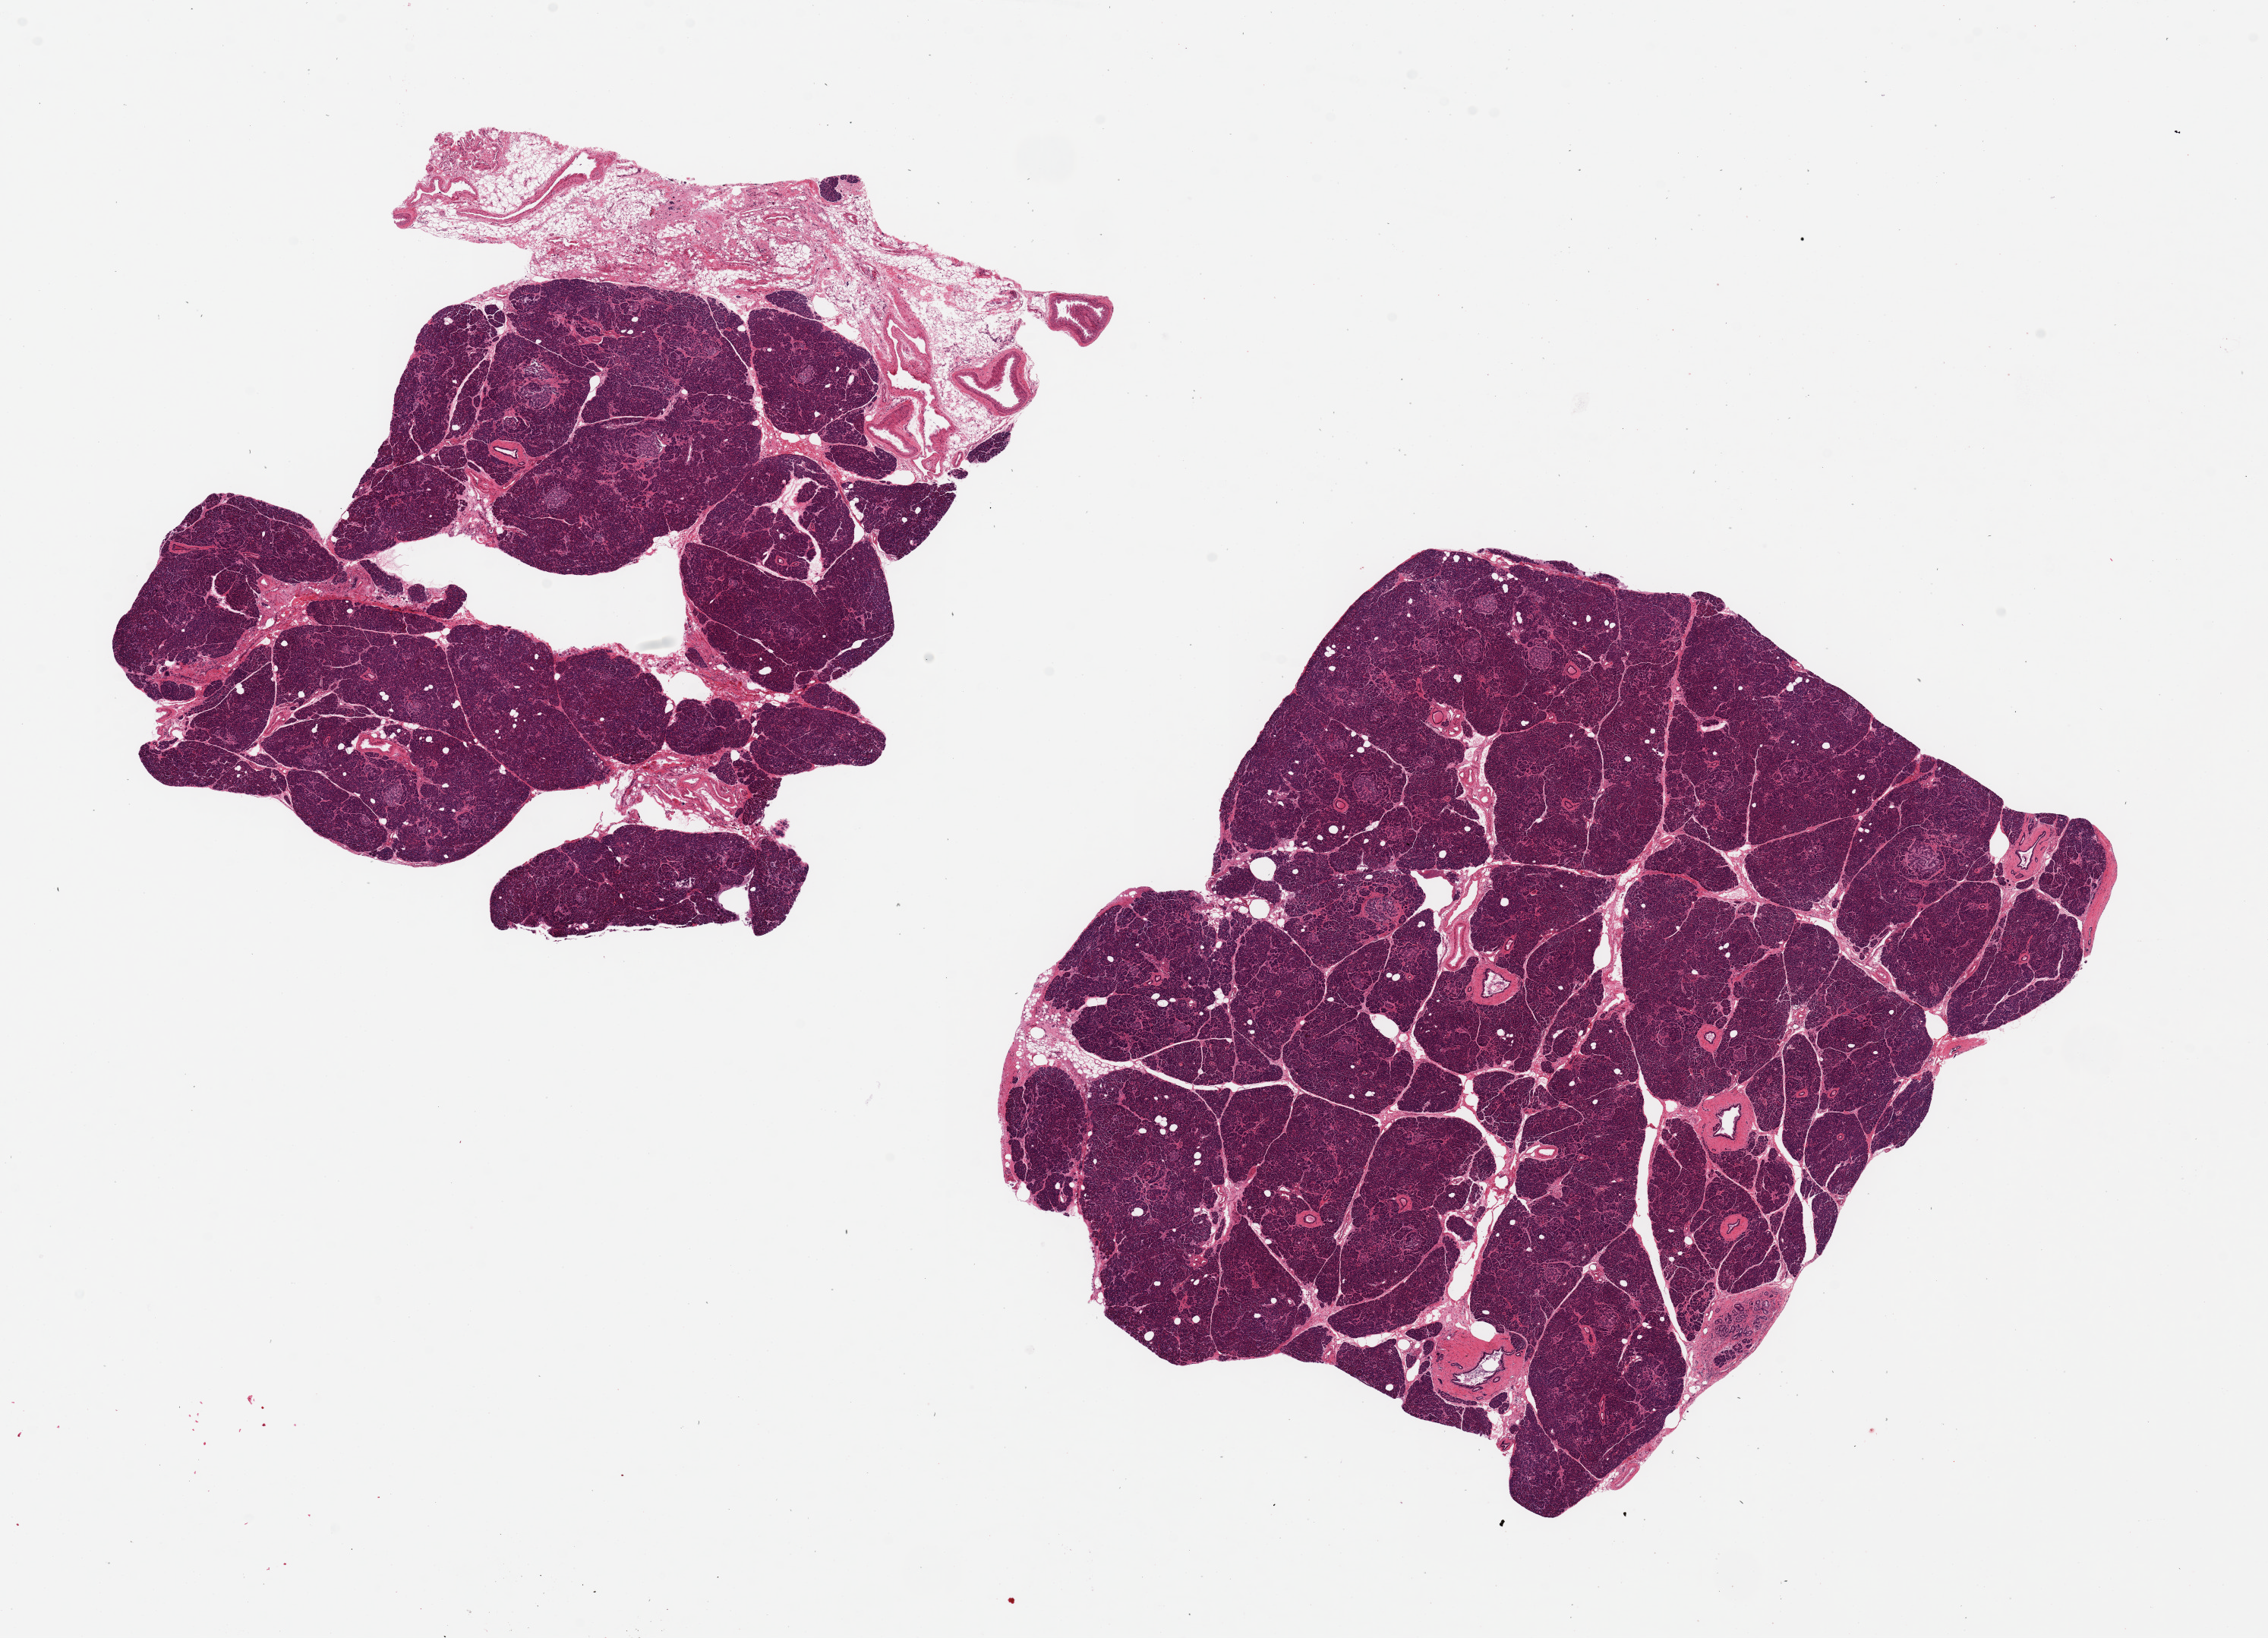
Whole-slide image, H&E stain, brightfield, whole scanned area (about 23.6 x 17.1 mm, from a 20x scan) shown as a low-resolution overview. PAXgene-fixed, paraffin-embedded tissue. Target tissue: pancreas. Tissue donor sample. Female donor.
- review note (as recorded): 2 pieces, 8x7.5 & 9x8mm; 1 mm adipose along one side of the smaller piece